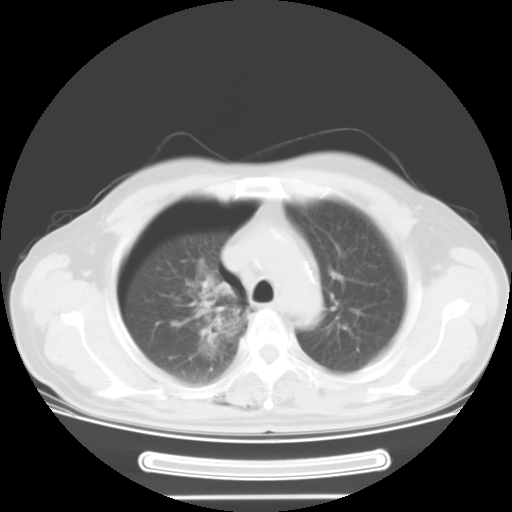
Chest CT, one axial slice. Slice 22 of 29 in the series (ordered by position). Reconstruction kernel STANDARD. 120 kVp. Lung window (W 1500 / L -600 HU). 10 mm slice thickness. 512 × 512 image matrix. Male patient, age 61 years. Case-level facts recorded for this patient, not image findings: clinical TNM (as recorded): T1c N3 M1b.
Annotated regions visible in this slice (rectangle marked by the reading radiologist):
- lung tumour (recorded histology: adenocarcinoma): bounding box (x1, y1, x2, y2) in pixels: (172, 263, 254, 371)